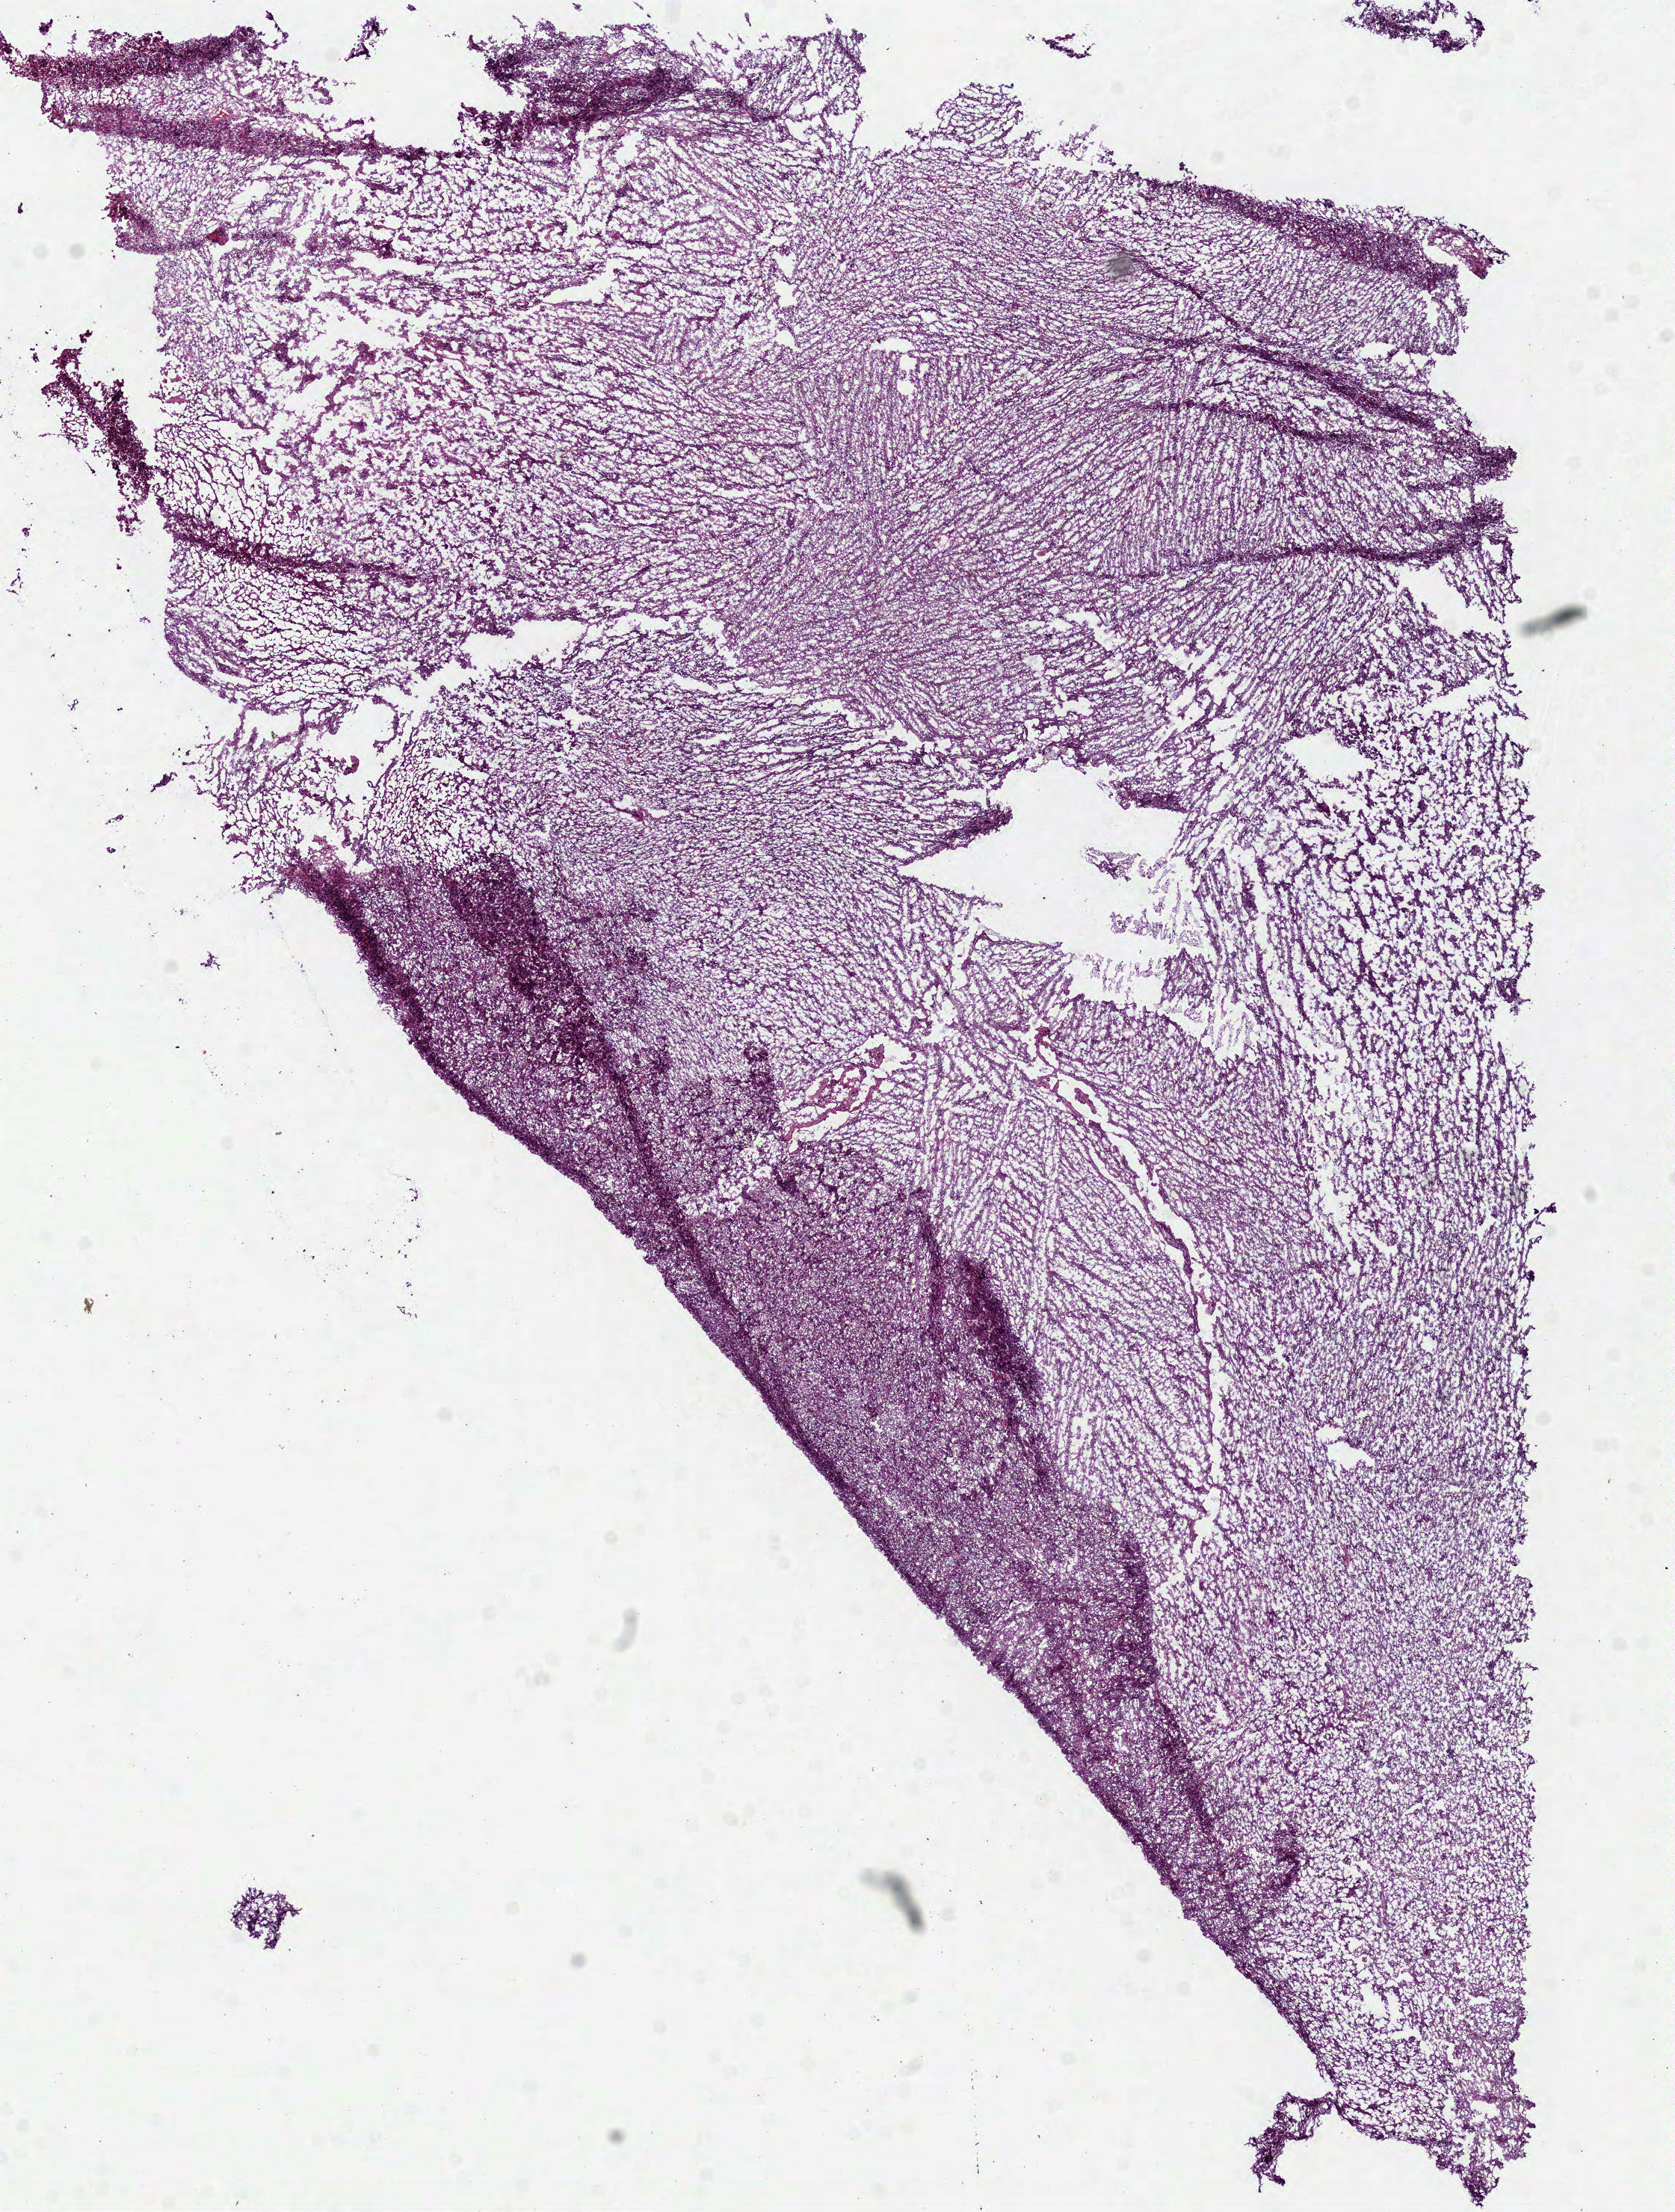
Whole-slide histology image, H&E-stained, a low-resolution overview of the entire scanned area, about 9.0 x 11.9 mm (slide scanned at 40x), frozen section from the bottom of the tissue portion, primary tumour sample from the brain. Male, age 66 years at initial diagnosis.
Pathologic diagnosis: Glioblastoma.